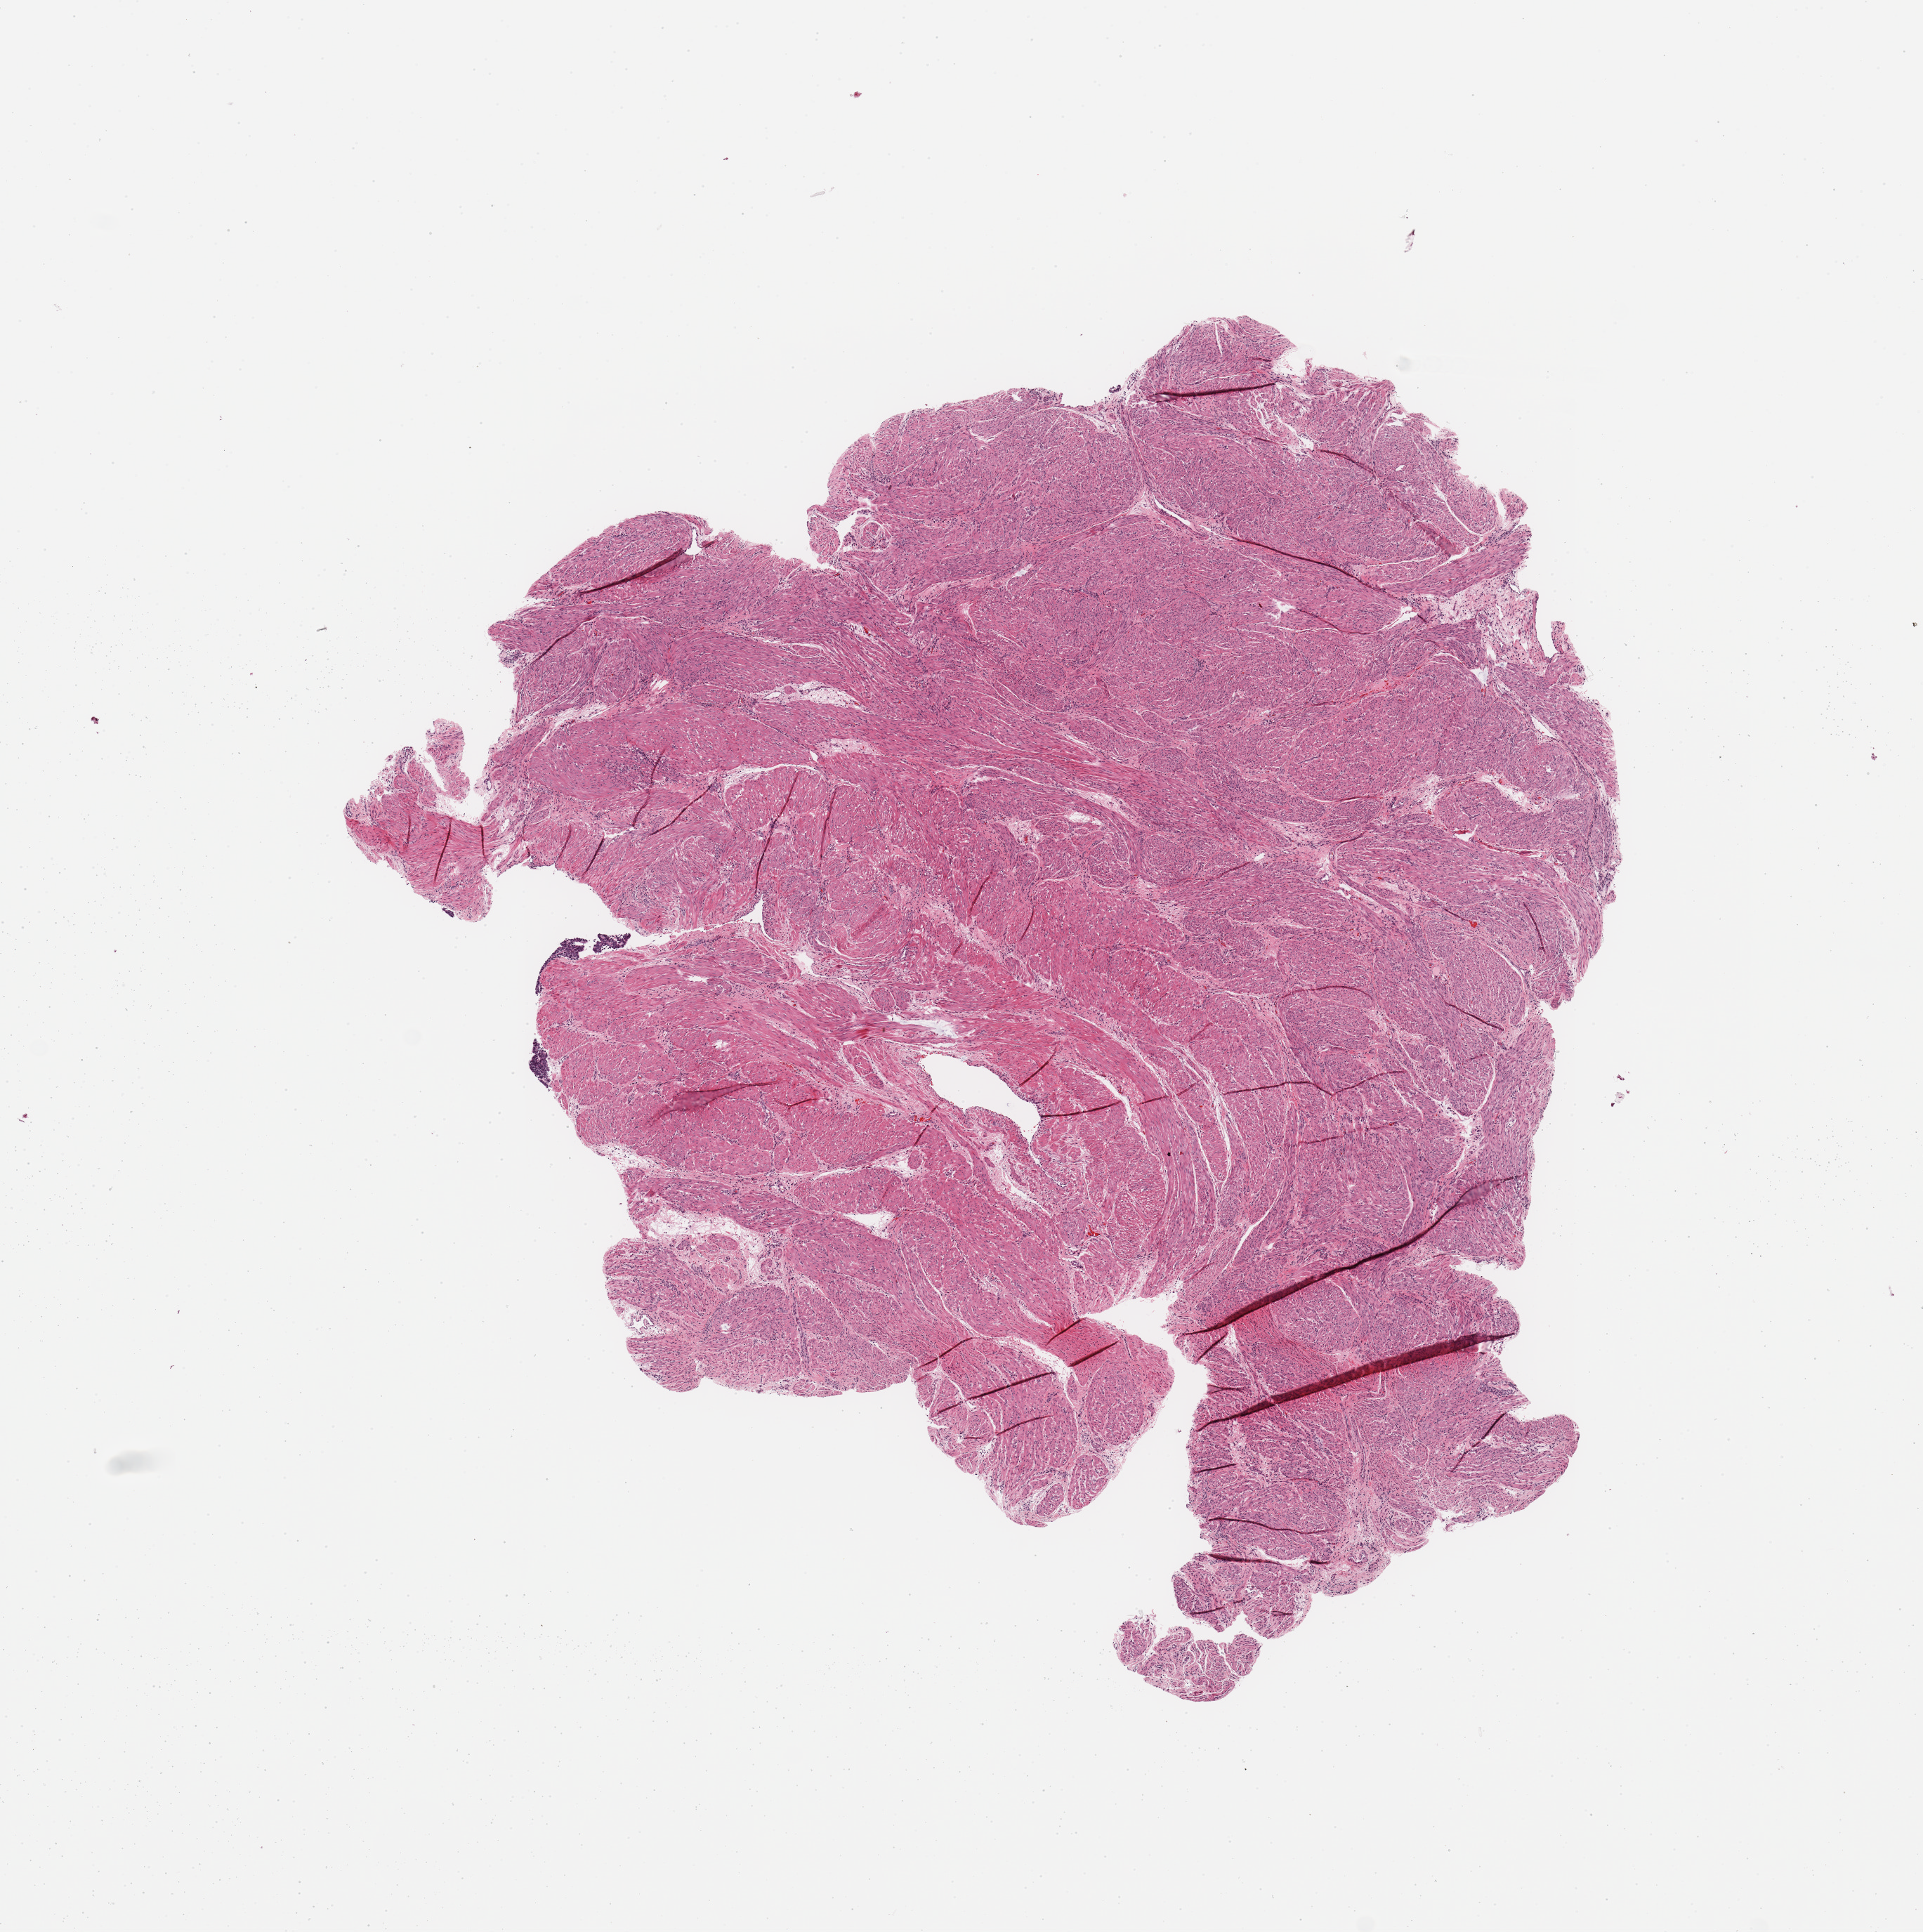
Digitized H&E tissue section (whole slide), a low-resolution overview of the entire scanned area, about 10.8 x 10.9 mm (from a 20x scan). Uterus, normal (non-tumour) tissue. Patient: female, age 55 years.
This section: normal (non-tumour) tissue from the same patient. Patient diagnosis: Endometrioid adenocarcinoma, NOS.